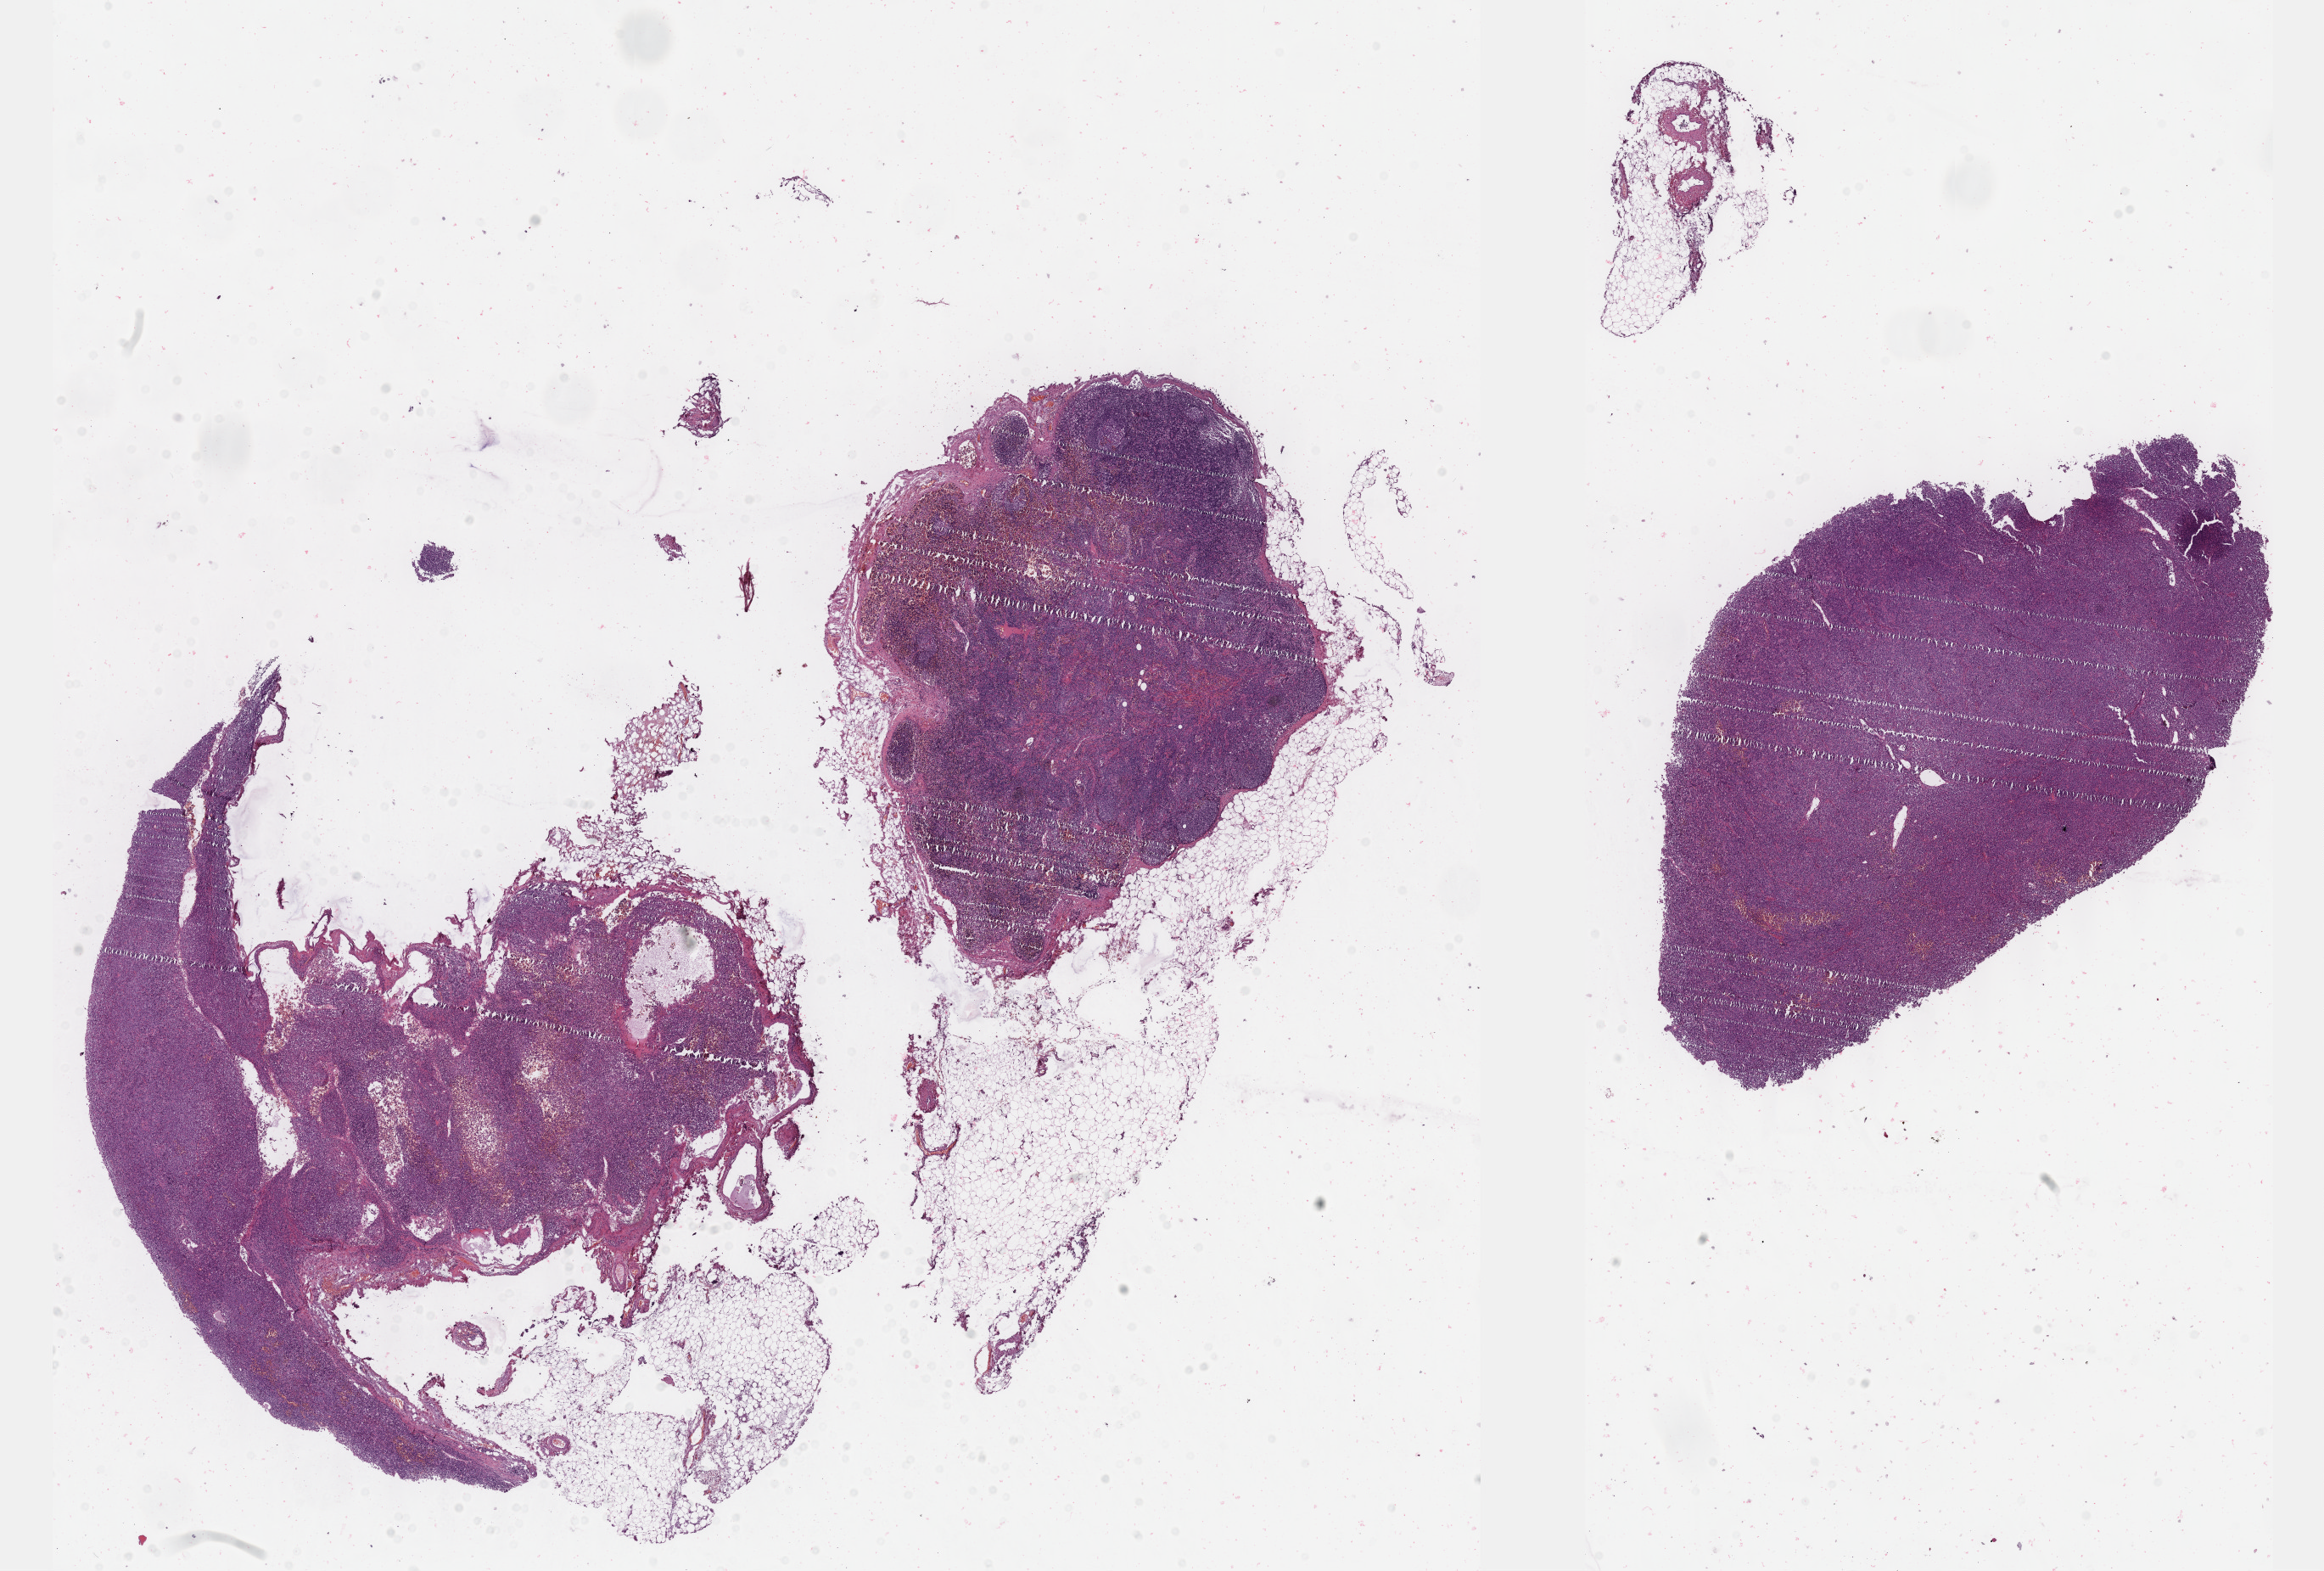
H&E whole-slide image — low-resolution overview of the scanned area, about 22.1 x 15.0 mm (slide scanned at 40x), FFPE section, lymphoid tissue, primary tumour sample. Male, age 45 years at initial diagnosis.
Pathologic diagnosis: Diffuse large B-cell lymphoma, NOS (lymph nodes of inguinal region or leg).